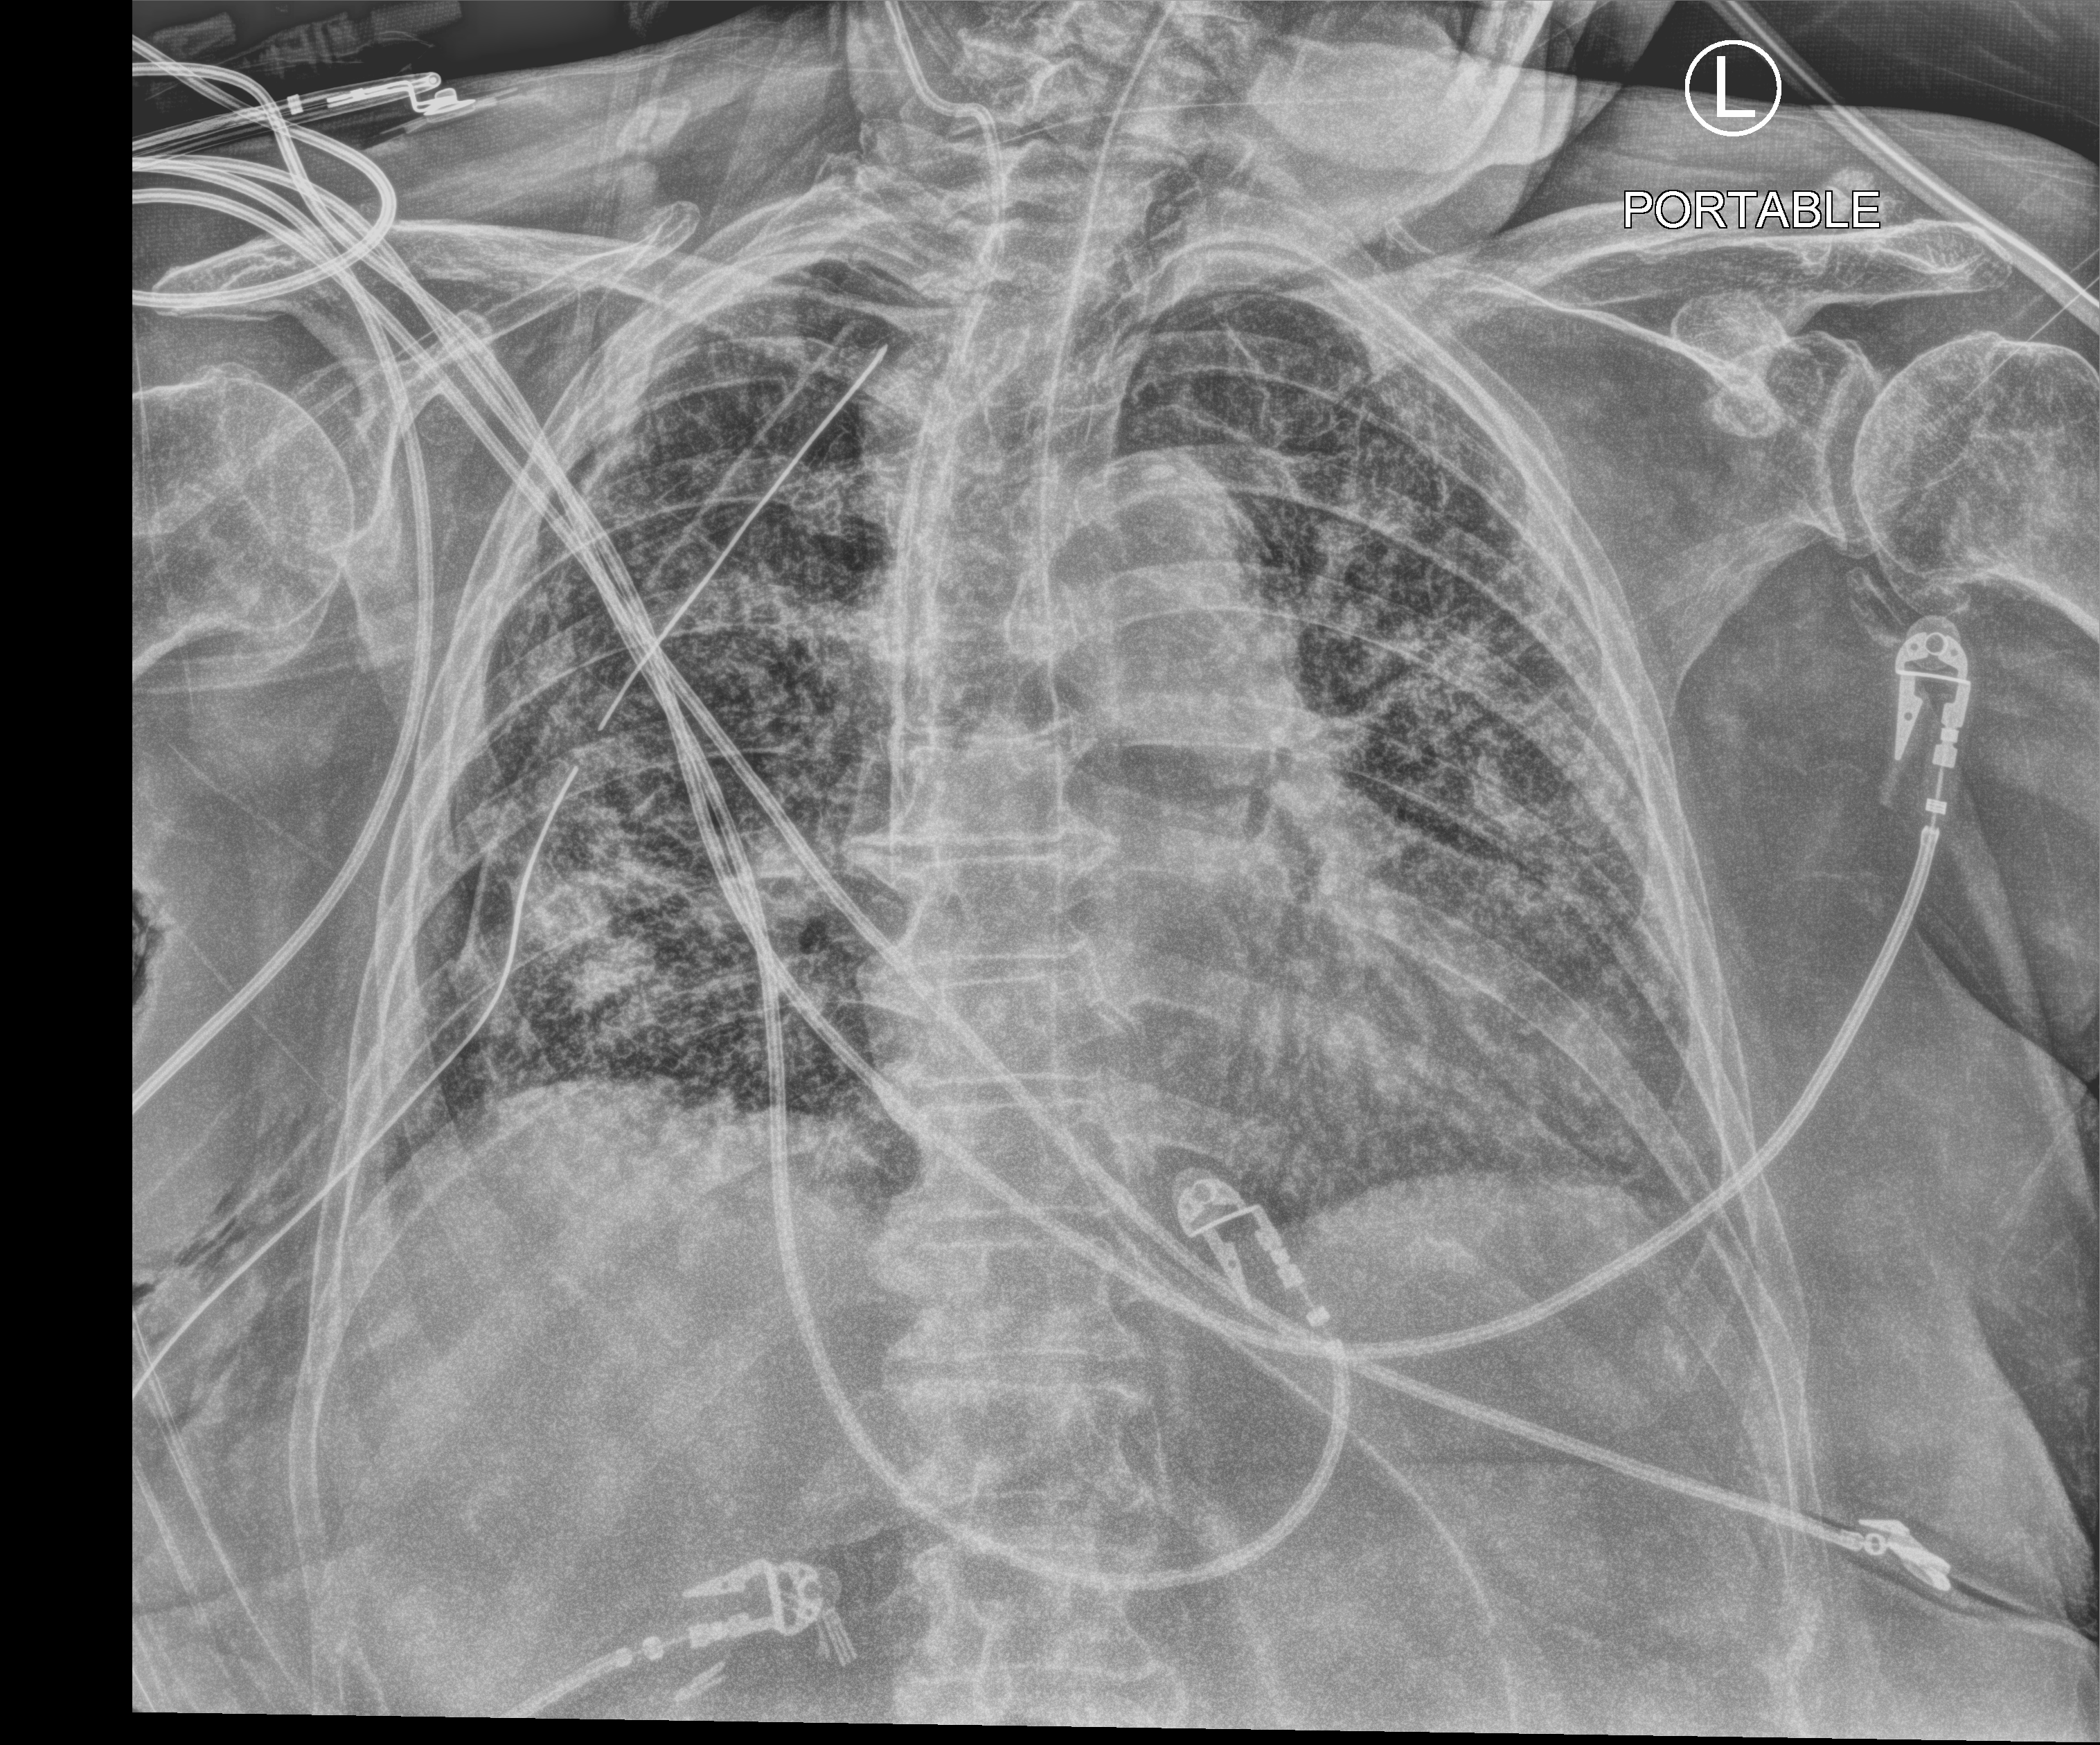
Portable chest radiograph. Female patient hospitalised with COVID-19, age 75–90 years.
Admission-level facts for this patient (not findings on this image; timing relative to this image not recorded): length of hospital stay: 56 days; mechanically ventilated during this hospital stay: yes.